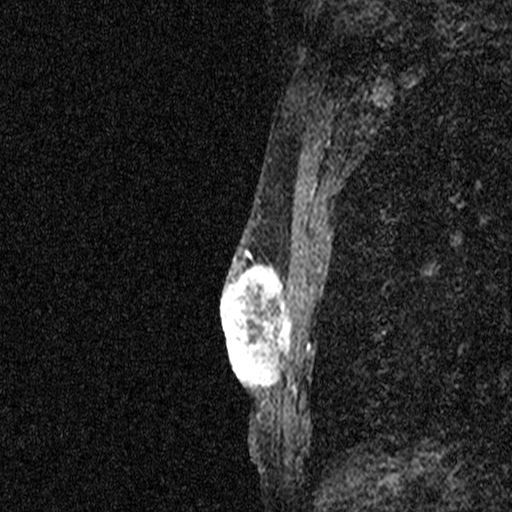
Breast MRI (dynamic contrast-enhanced), one sagittal slice; slice 30 of 44 in the series (ordered by position); dynamic contrast-enhanced study with each time point stored as its own series, time point 2 of 3 at this slice position (early post-contrast, ordered by acquisition time); 1.5 T; TE 4.5 ms, TR 11 ms; 2.05 mm slice thickness; 512 × 512 image matrix. Patient: female, 44 years. Case-level facts recorded for this patient, not image findings: setting: breast cancer imaged before/during neoadjuvant chemotherapy; receptor status: HR-positive, HER2-negative.
Annotated regions visible in this slice (semi-automatically segmented with operator editing):
- analysis volume of interest (the breast-tissue region the enhancement analysis was run in; not a lesion): bounding box (x1, y1, x2, y2) in pixels: (204, 254, 296, 401)
- tumour enhancement mask (voxels above the 90 % enhancement threshold inside the analysis volume of interest): (221, 254, 291, 394)